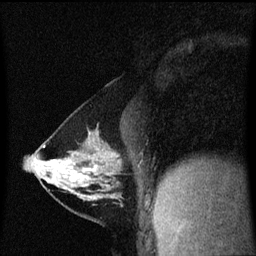
Breast MRI (dynamic contrast-enhanced), one sagittal slice. Position 29 of 60 along the scan axis. Dynamic contrast-enhanced series, image 2 of 3 at this slice position (ordered by acquisition). 1.5 T. TE 4.2 ms, TR 8.4 ms. 256 × 256 image matrix, field of view 200 × 200 mm. Female patient, age 40 years. Case-level facts recorded for this patient, not image findings: setting: breast cancer imaged before/during neoadjuvant chemotherapy; receptor status: triple-negative.
Outlined on this slice (semi-automatically segmented with operator editing):
- analysis volume of interest (the breast-tissue region the enhancement analysis was run in; not a lesion): bounding box (x1, y1, x2, y2) in pixels: (34, 142, 122, 199)
- tumour enhancement mask (voxels above the 70 % enhancement threshold inside the analysis volume of interest): (84, 166, 96, 171)